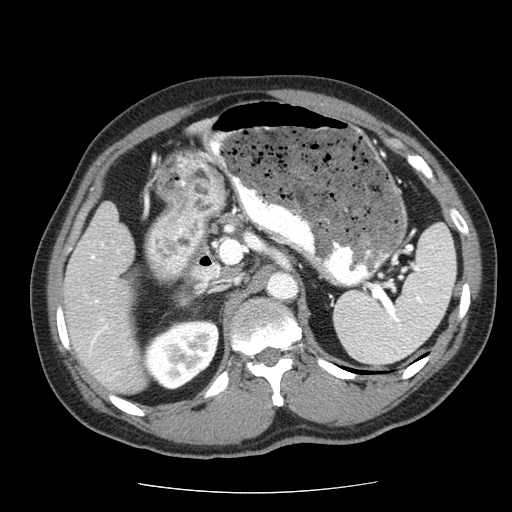
Contrast-enhanced abdominal CT (liver protocol), one axial slice; position 26 of 85 along the scan axis; reconstruction kernel STANDARD; 120 kVp; soft-tissue window (W 400 / L 40 HU); 2.5 mm slice thickness; 512 × 512 image matrix. Case-level facts recorded for this patient, not image findings: diagnosis: hepatocellular carcinoma (patient treated with transarterial chemoembolisation; whether this scan precedes or follows treatment is not stated here); TNM stage (as recorded): Stage-IIIA; Child-Pugh class: A; tumour differentiation: well differentiated; tumour size: 8 cm.
Outlined on this slice (semi-automatically segmented with operator editing):
- liver parenchyma outside the tumour (the mass and vessels are separate outlines, so this box may not span the whole liver): bounding box <63,202,148,394> (left, top, right, bottom; pixels)
- liver vessels: <89,242,119,374>